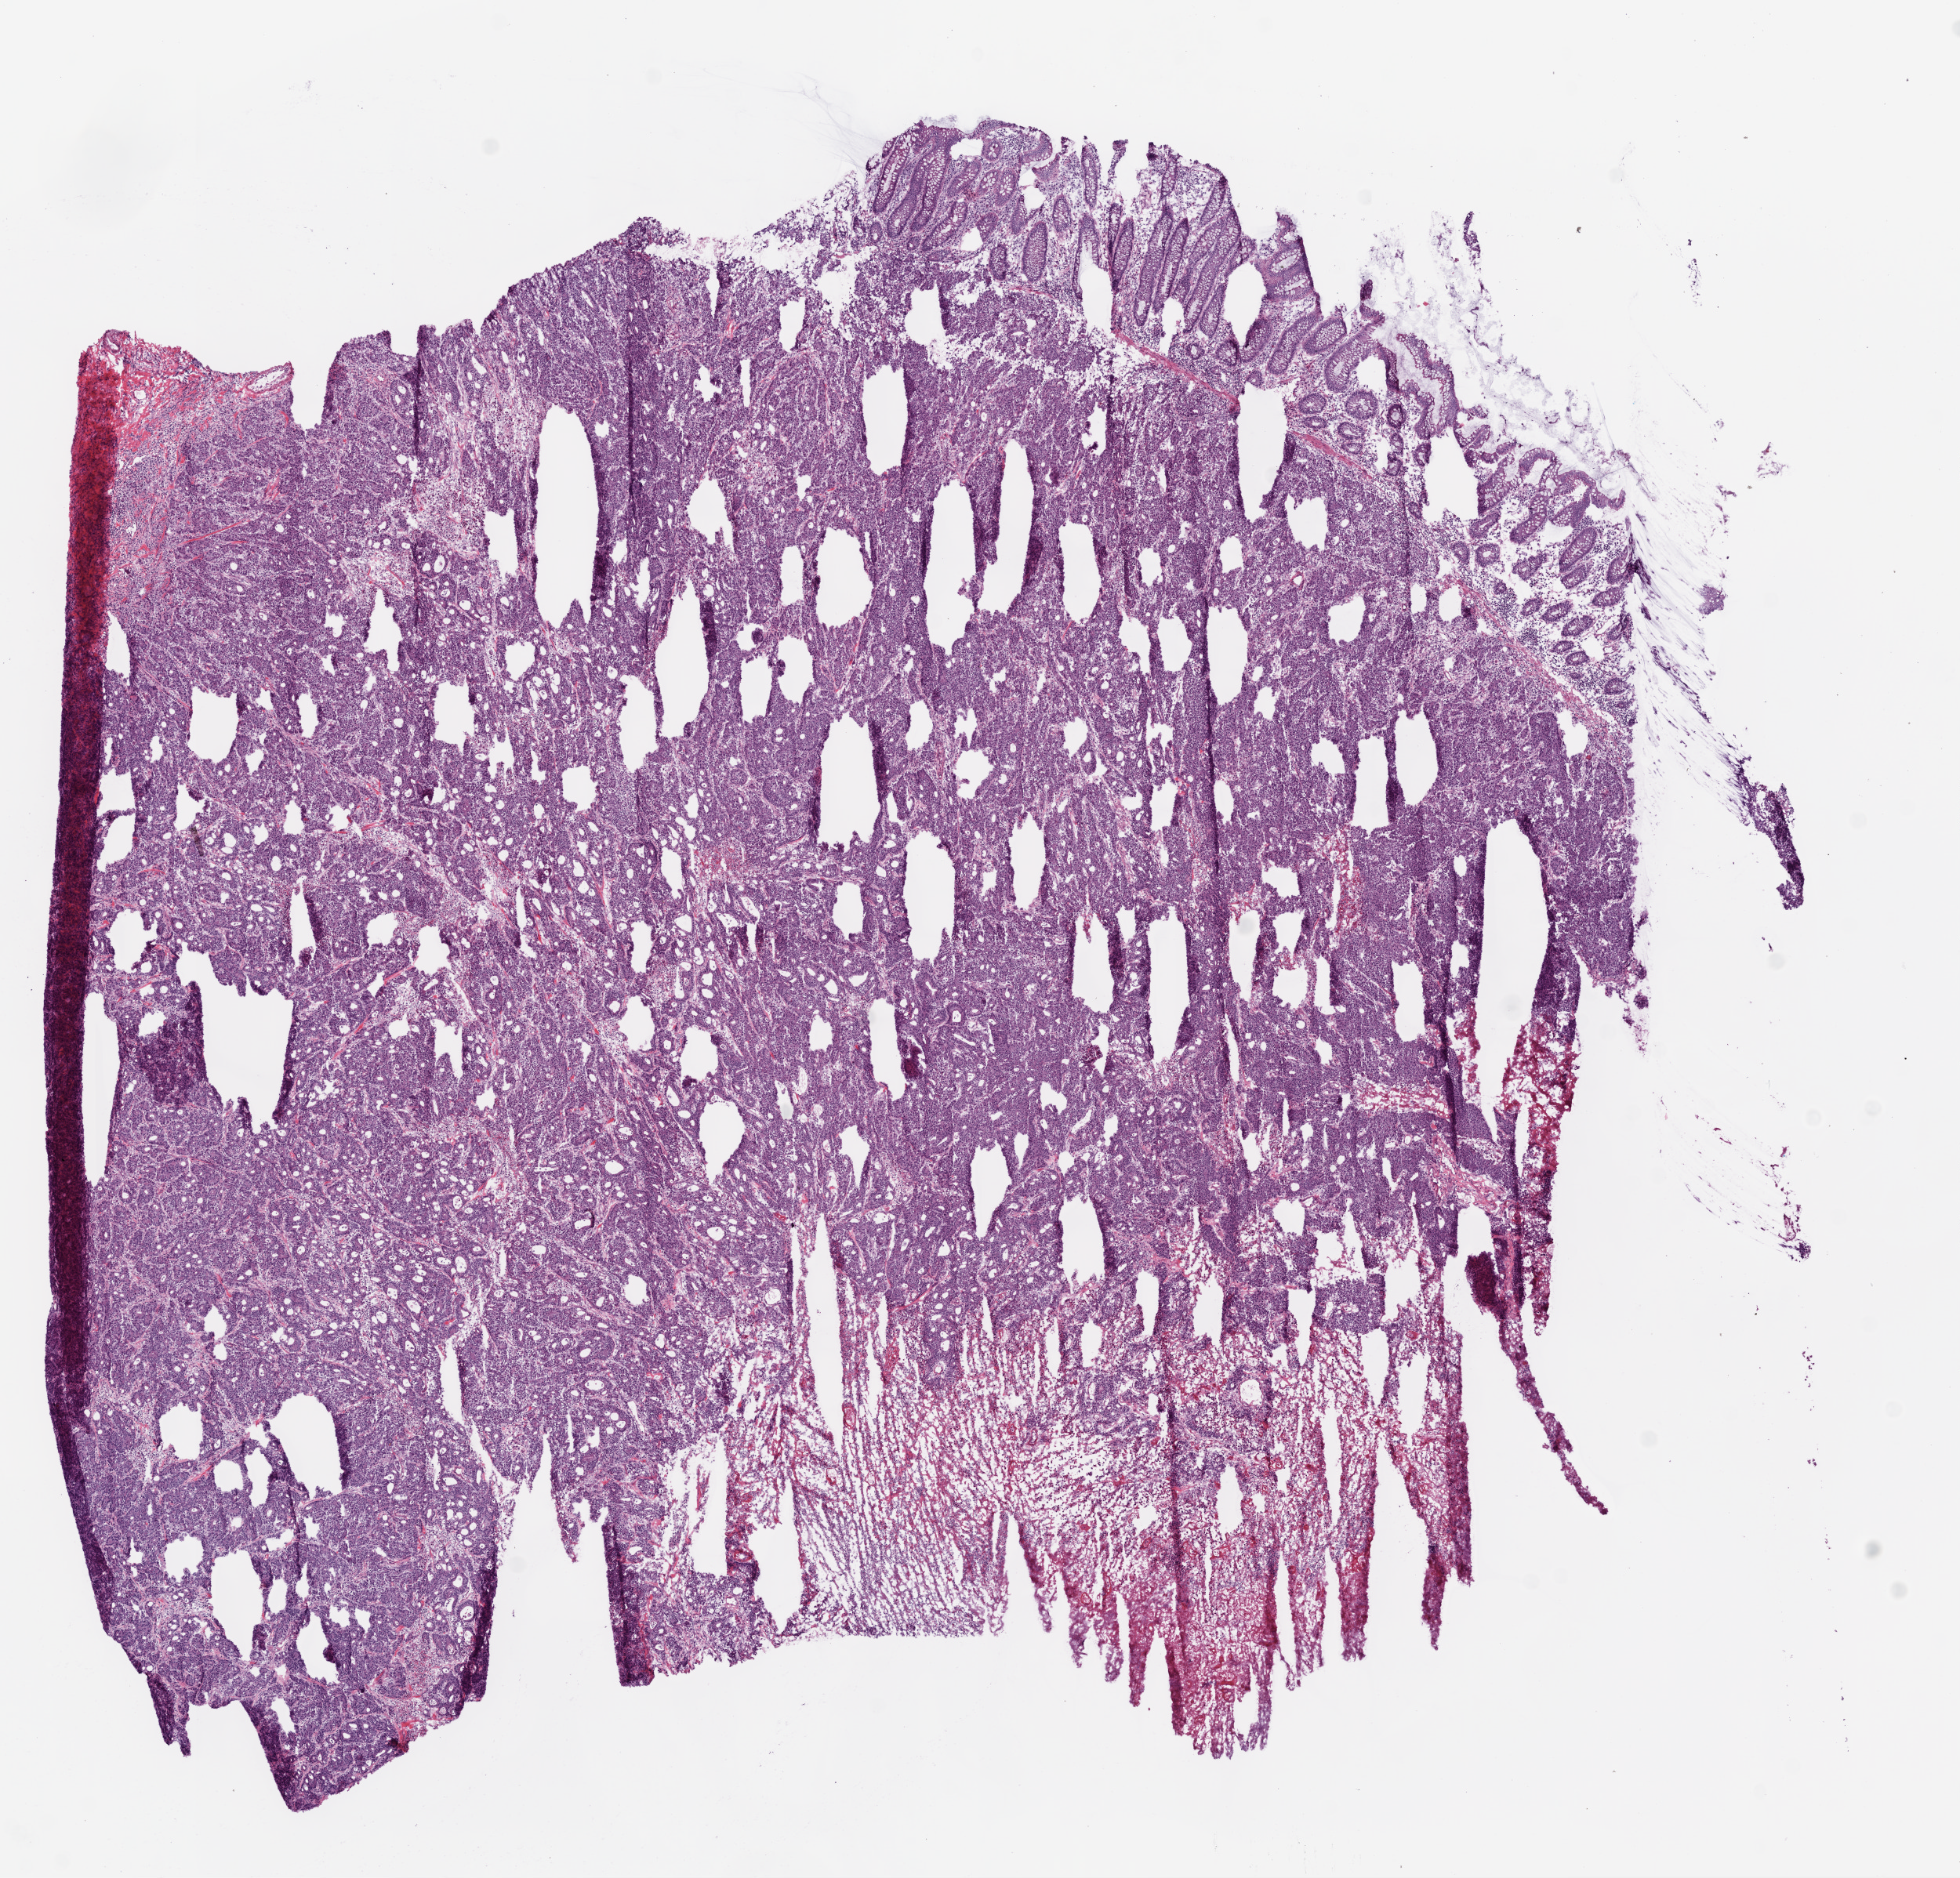
Whole-slide histology image, Hematoxylin and eosin (H&E) stained — a low-resolution overview of the entire scanned area, about 10.0 x 9.6 mm (acquisition: 20x scan), frozen section from the bottom of the tissue portion, primary tumour sample from the colon. Patient sex: female. Composition of this section per pathologist review: tumour cells 85%, tumour nuclei 90%, normal cells 2%, stromal cells 8%, necrosis 5%.
- TNM: T3 N1 M0
- pathologic diagnosis: Adenocarcinoma, NOS
- AJCC pathologic stage: III (5th edition)